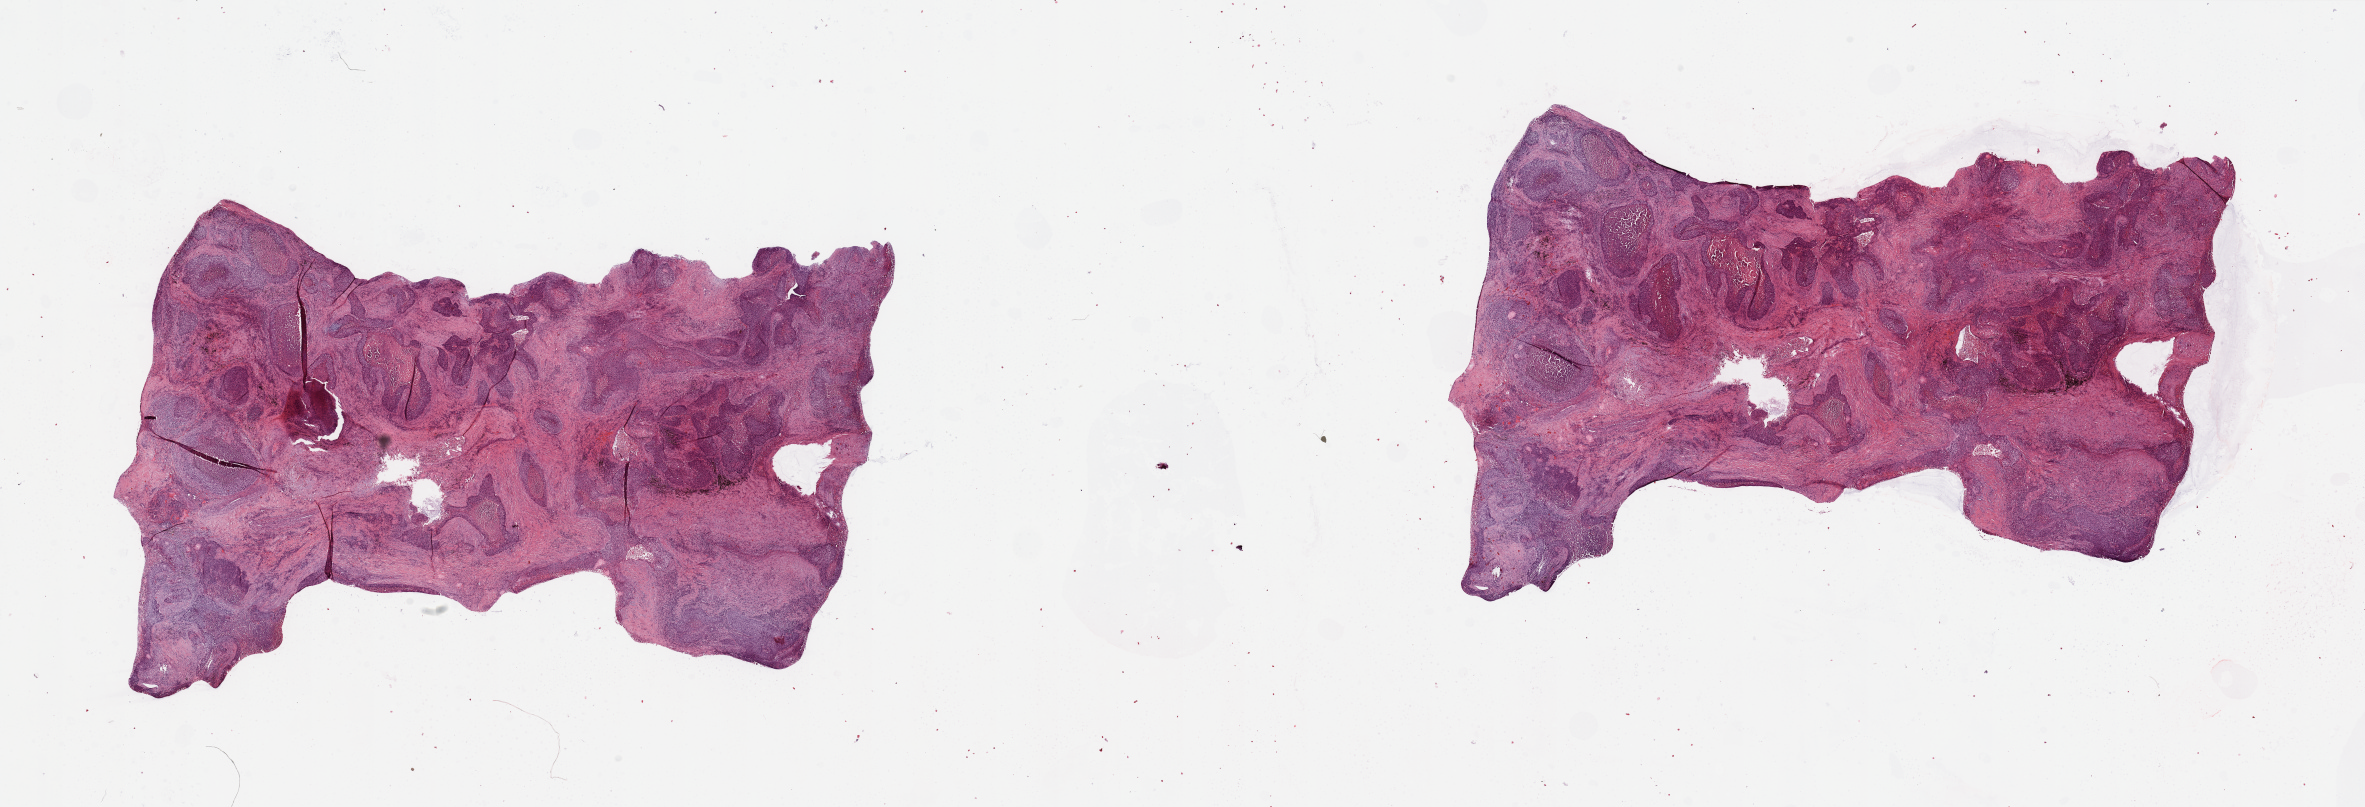
Hematoxylin and eosin (H&E) stained whole-slide image, whole scanned area (about 37.4 x 12.8 mm, from a 20x scan) shown as a low-resolution overview. Lung, tumour tissue. Patient: male, age 70 years. Histologic grade: G3 (poorly differentiated).
AJCC pathologic stage: IIIA. Histologic diagnosis: Squamous cell carcinoma, NOS. Primary tumour site (as recorded): right lower lobe.